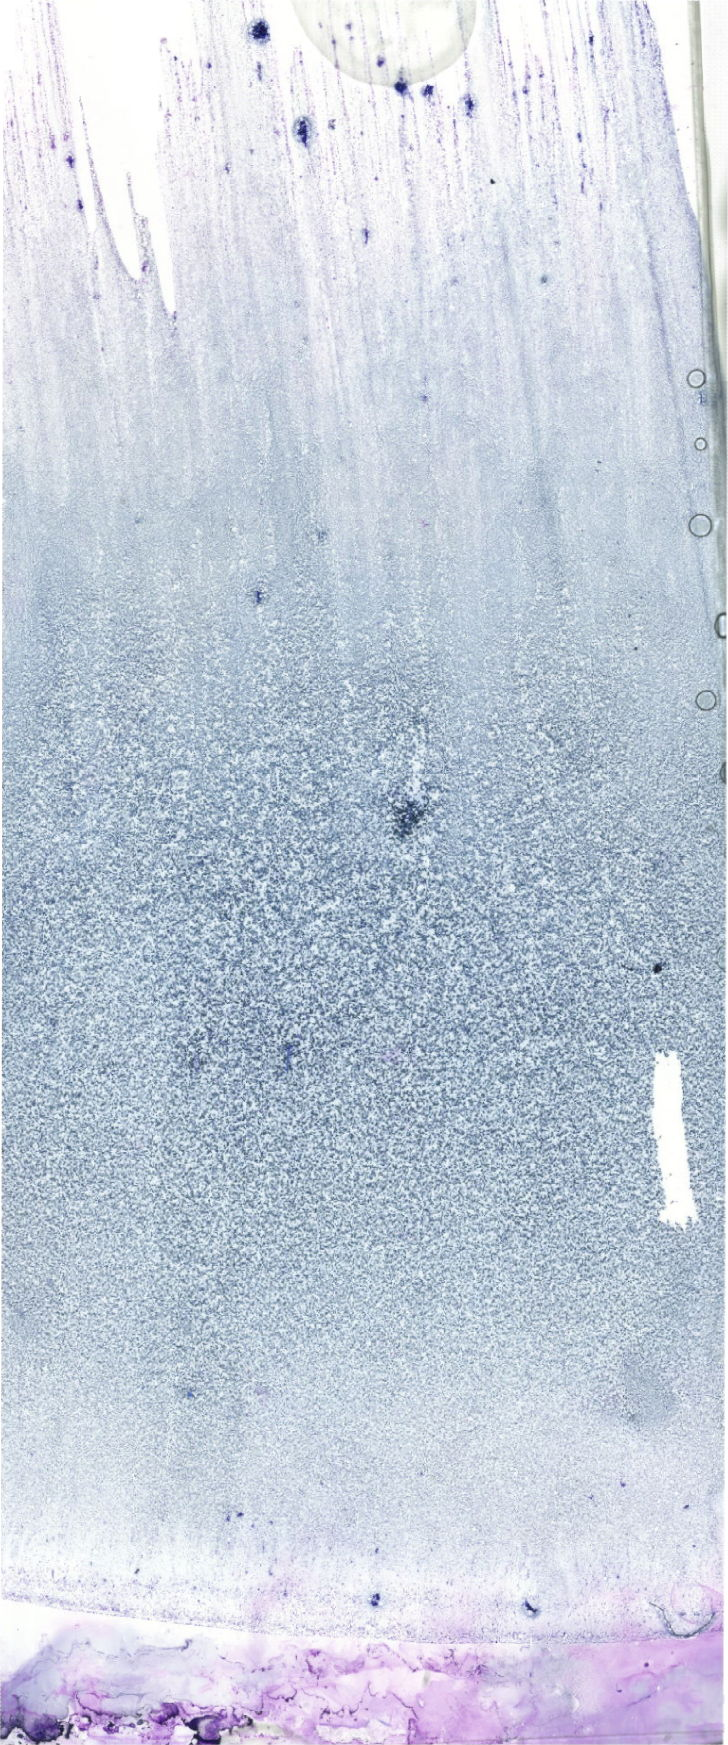
May-Grünwald-Giemsa (MGG)-stained marrow aspirate smear (whole slide), shown as a low-resolution overview of the whole scanned area (about 20.6 x 49.5 mm). Patient sex: male.
Diagnosis: B Acute Lymphoblastic Leukemia.